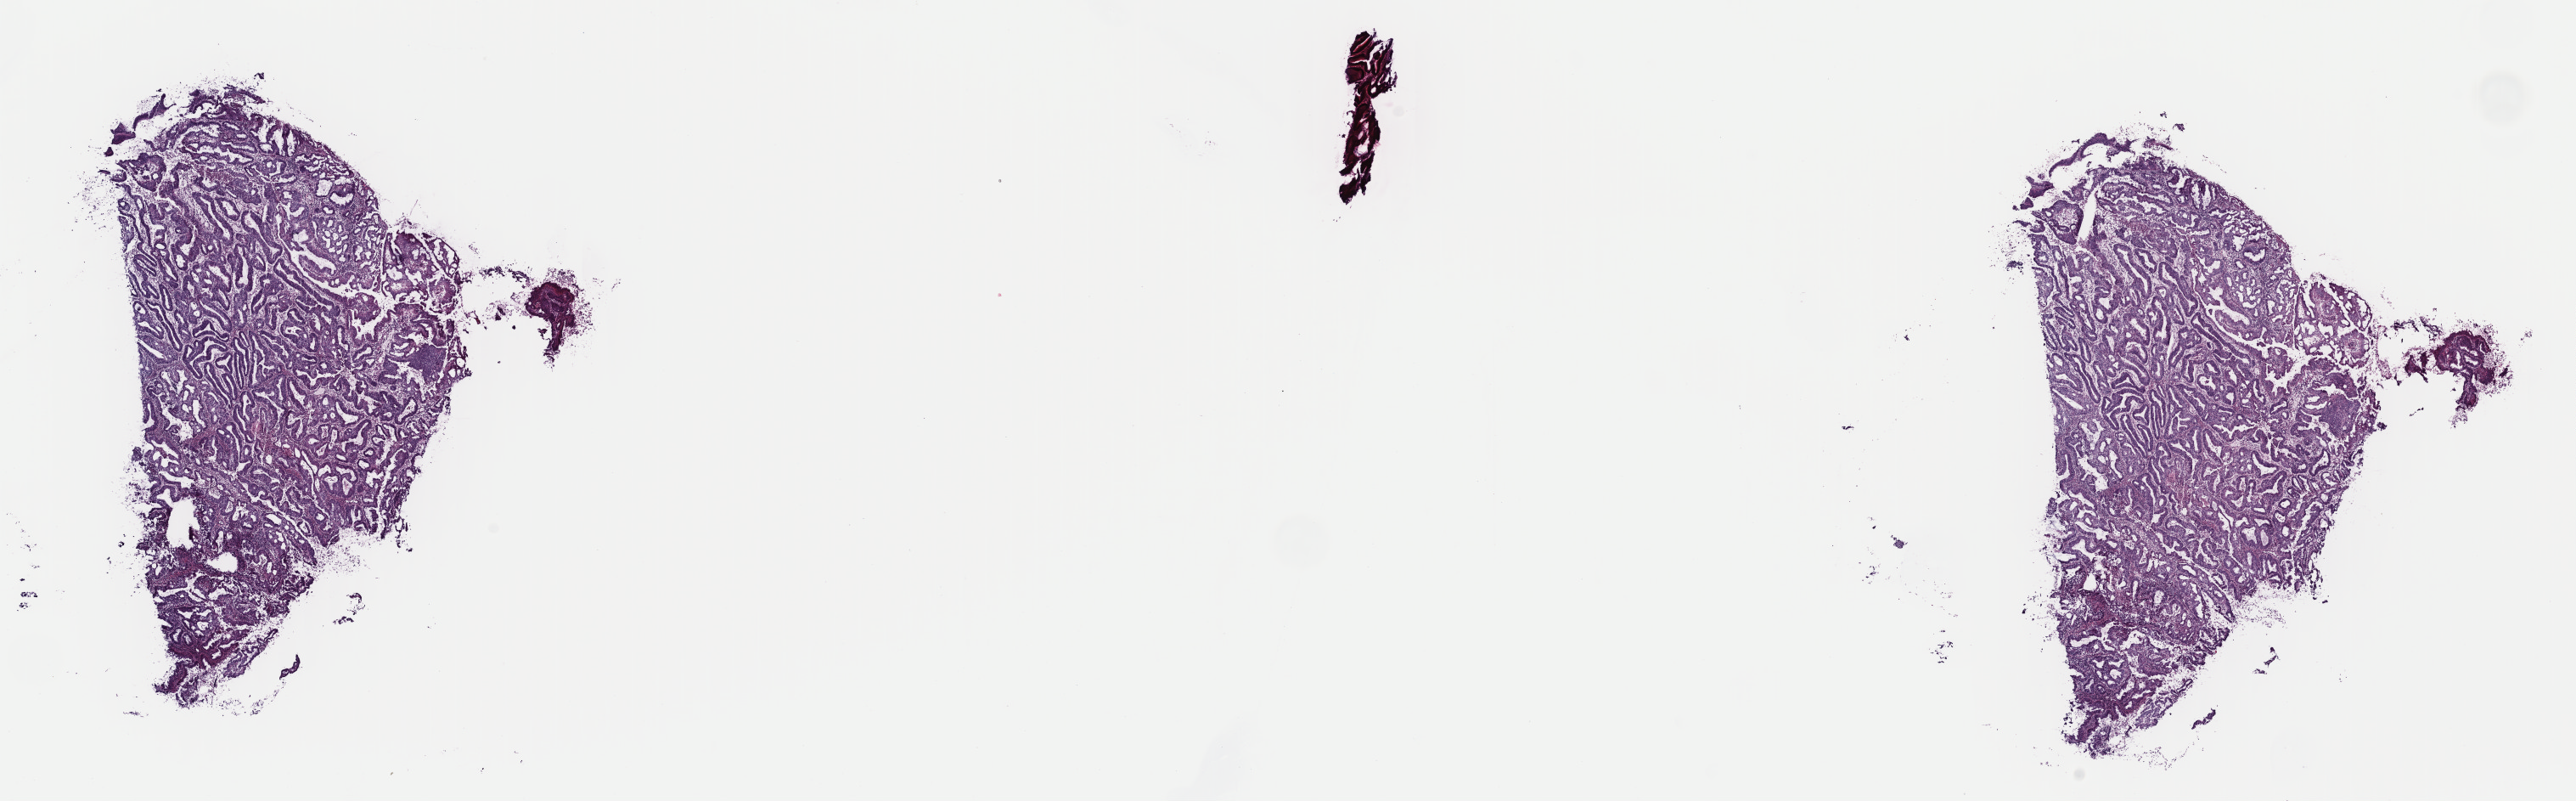
Whole-slide histology image, H&E-stained, whole scanned area (about 23.9 x 7.4 mm, from a 40x scan) shown as a low-resolution overview. Frozen section. Sample: primary tumour, uterus. Female, age 64 years at initial diagnosis. Histologic grade: G1 (well differentiated). Slide review estimates, as recorded: tumour cells 80%, tumour nuclei 80%, normal cells 0%, stromal cells 20%, necrosis 0%. Inflammatory infiltration, as recorded: lymphocyte infiltration 5%, monocyte infiltration 0%, neutrophil infiltration 0%.
* pathologic diagnosis: Endometrioid adenocarcinoma, NOS (endometrium)
* FIGO stage: IB